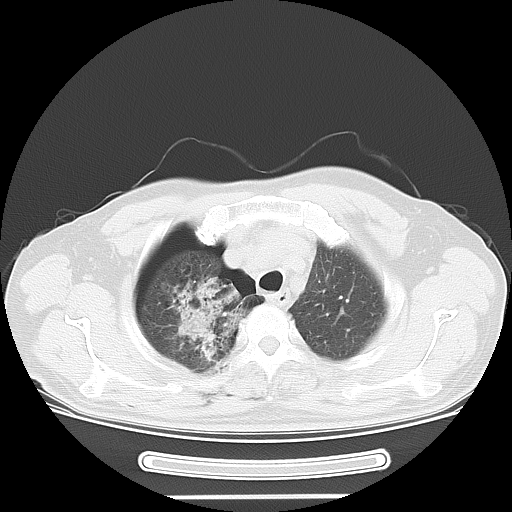
Chest CT, one axial slice; position 48 of 57 along the scan axis; 120 kVp; lung window (W 1500 / L -600 HU); 5 mm slice thickness; 512 × 512 image matrix. Patient: male, 61 years. From the clinical record (not read from this slice): clinical TNM (as recorded): T1c N3 M1b.
Annotated regions visible in this slice (bounding box drawn by a radiologist):
- lung tumour (recorded histology: adenocarcinoma): bounding box <165,275,243,362> (left, top, right, bottom; pixels)